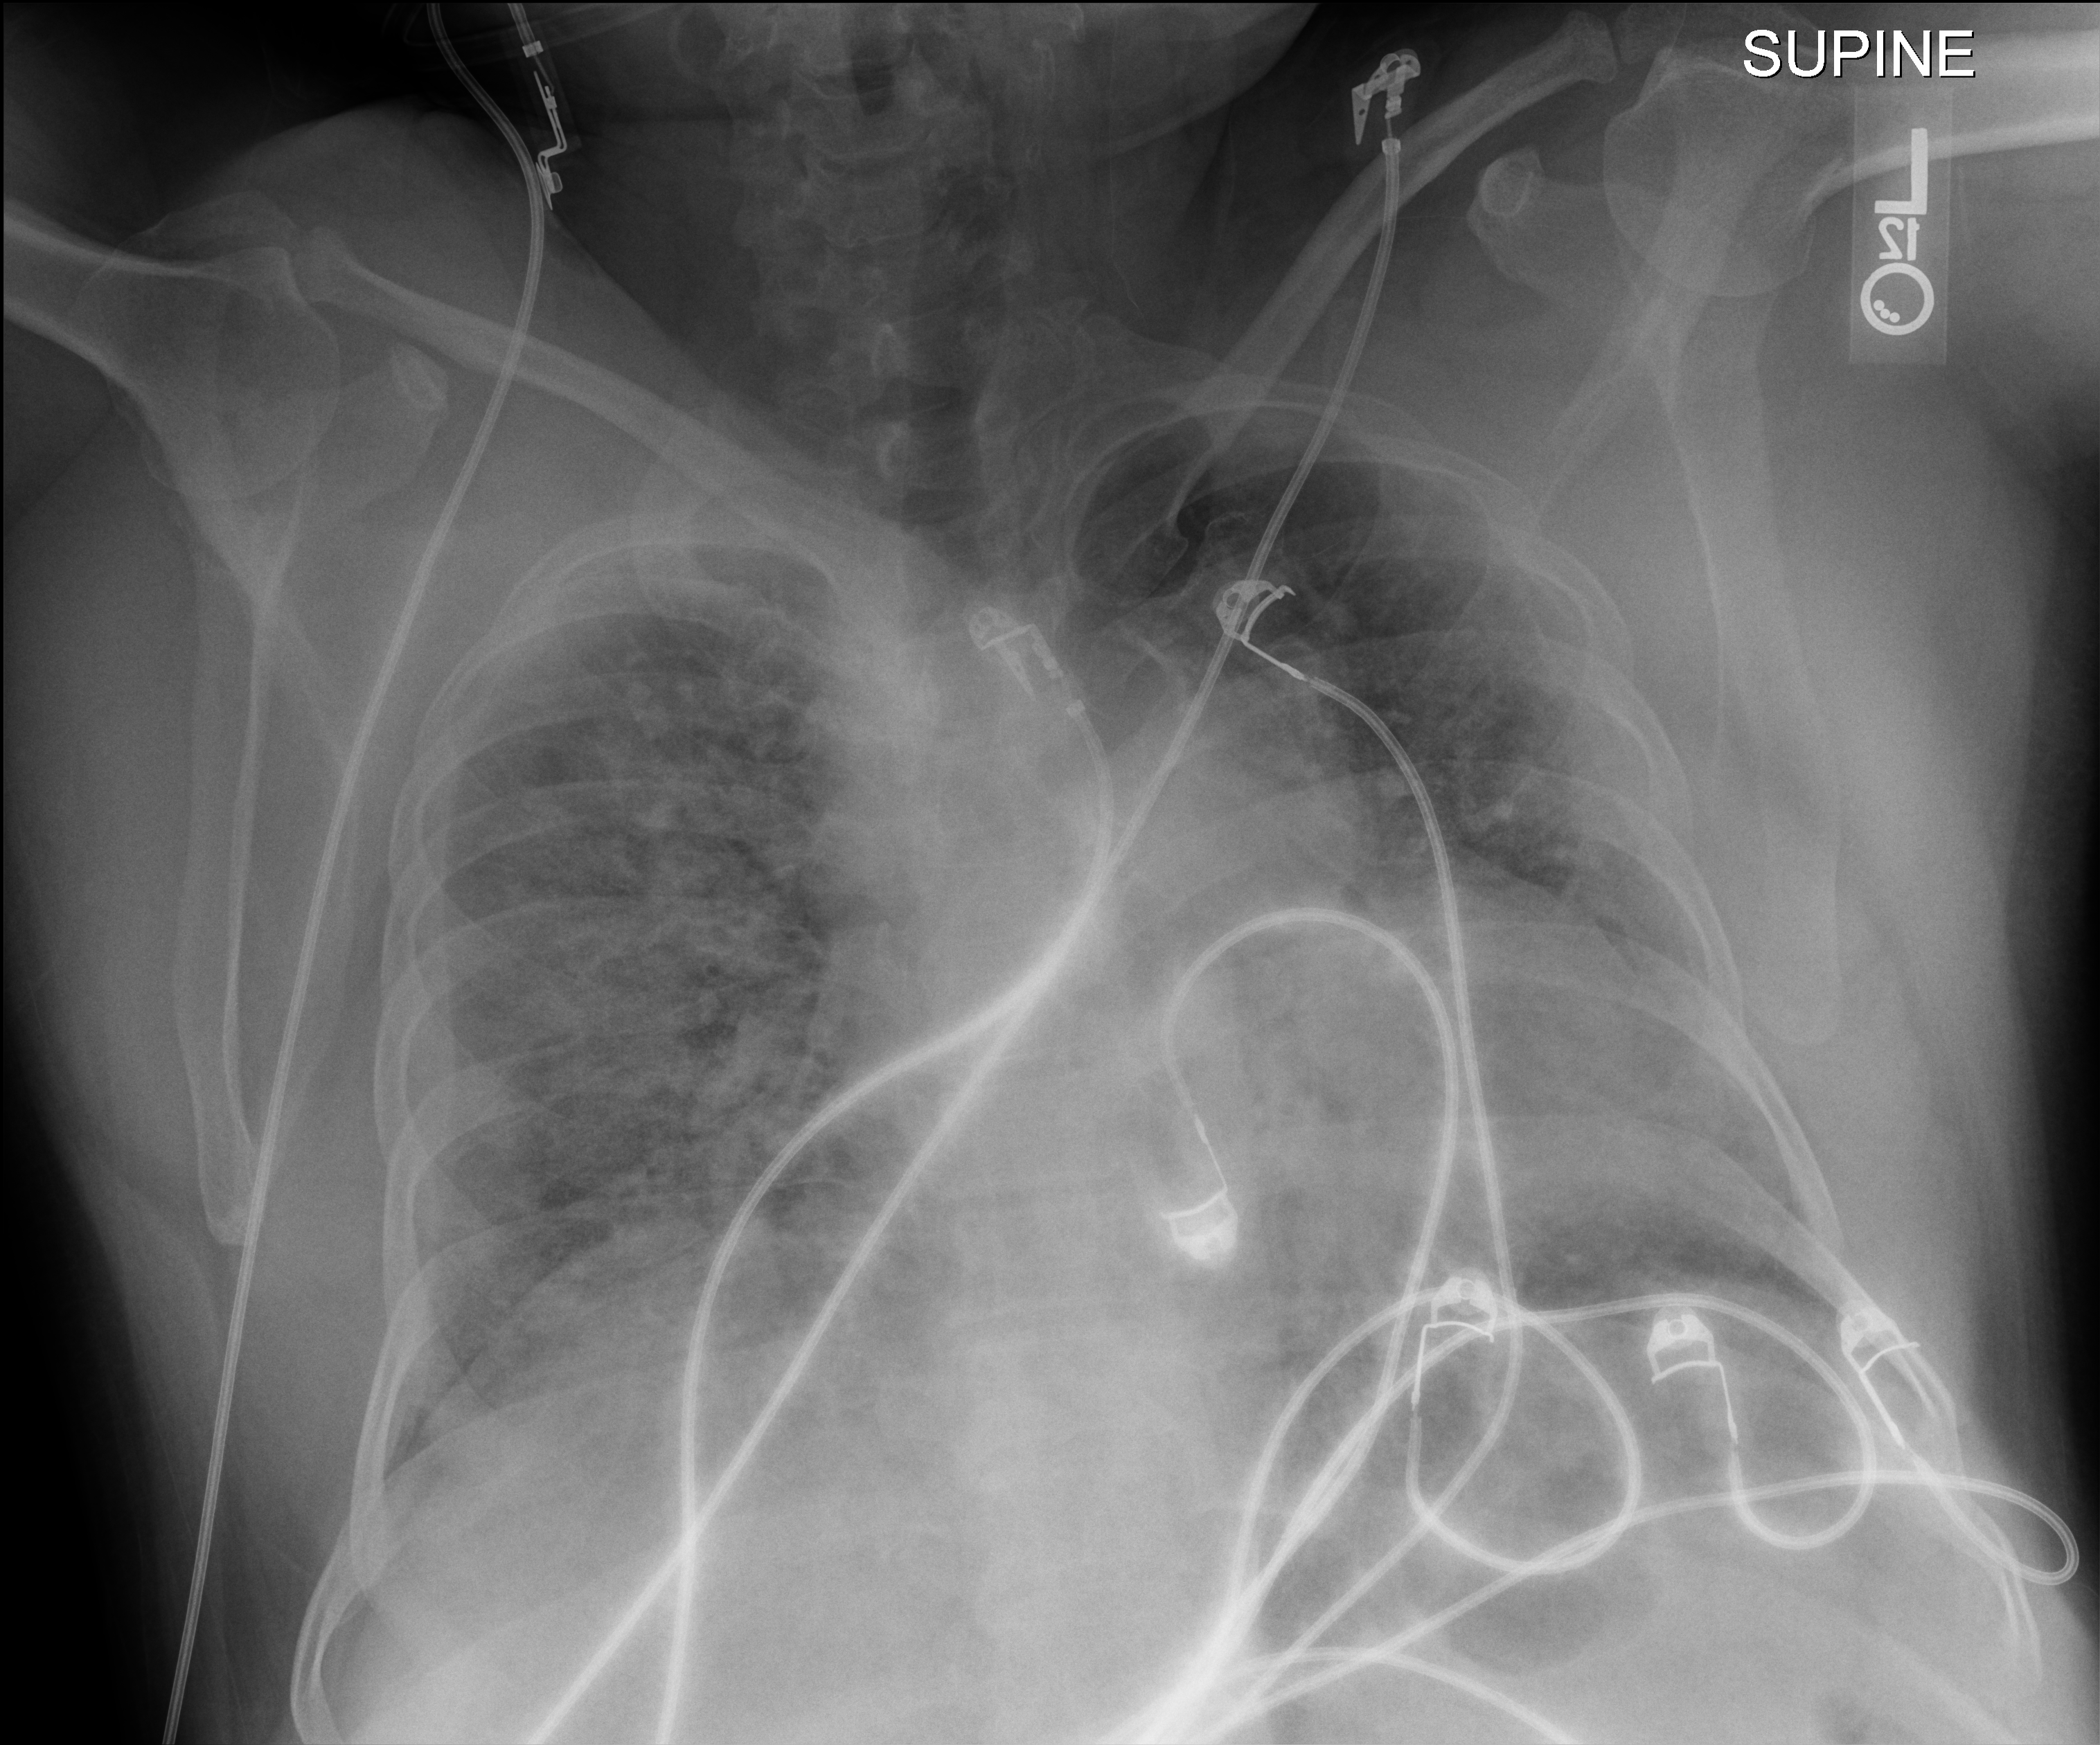
Chest X-ray; anteroposterior (AP) projection. Patient hospitalised with COVID-19, aged 18–59 years.
Admission-level facts for this patient (not findings on this image; timing relative to this image not recorded):
- mechanically ventilated during this hospital stay: yes